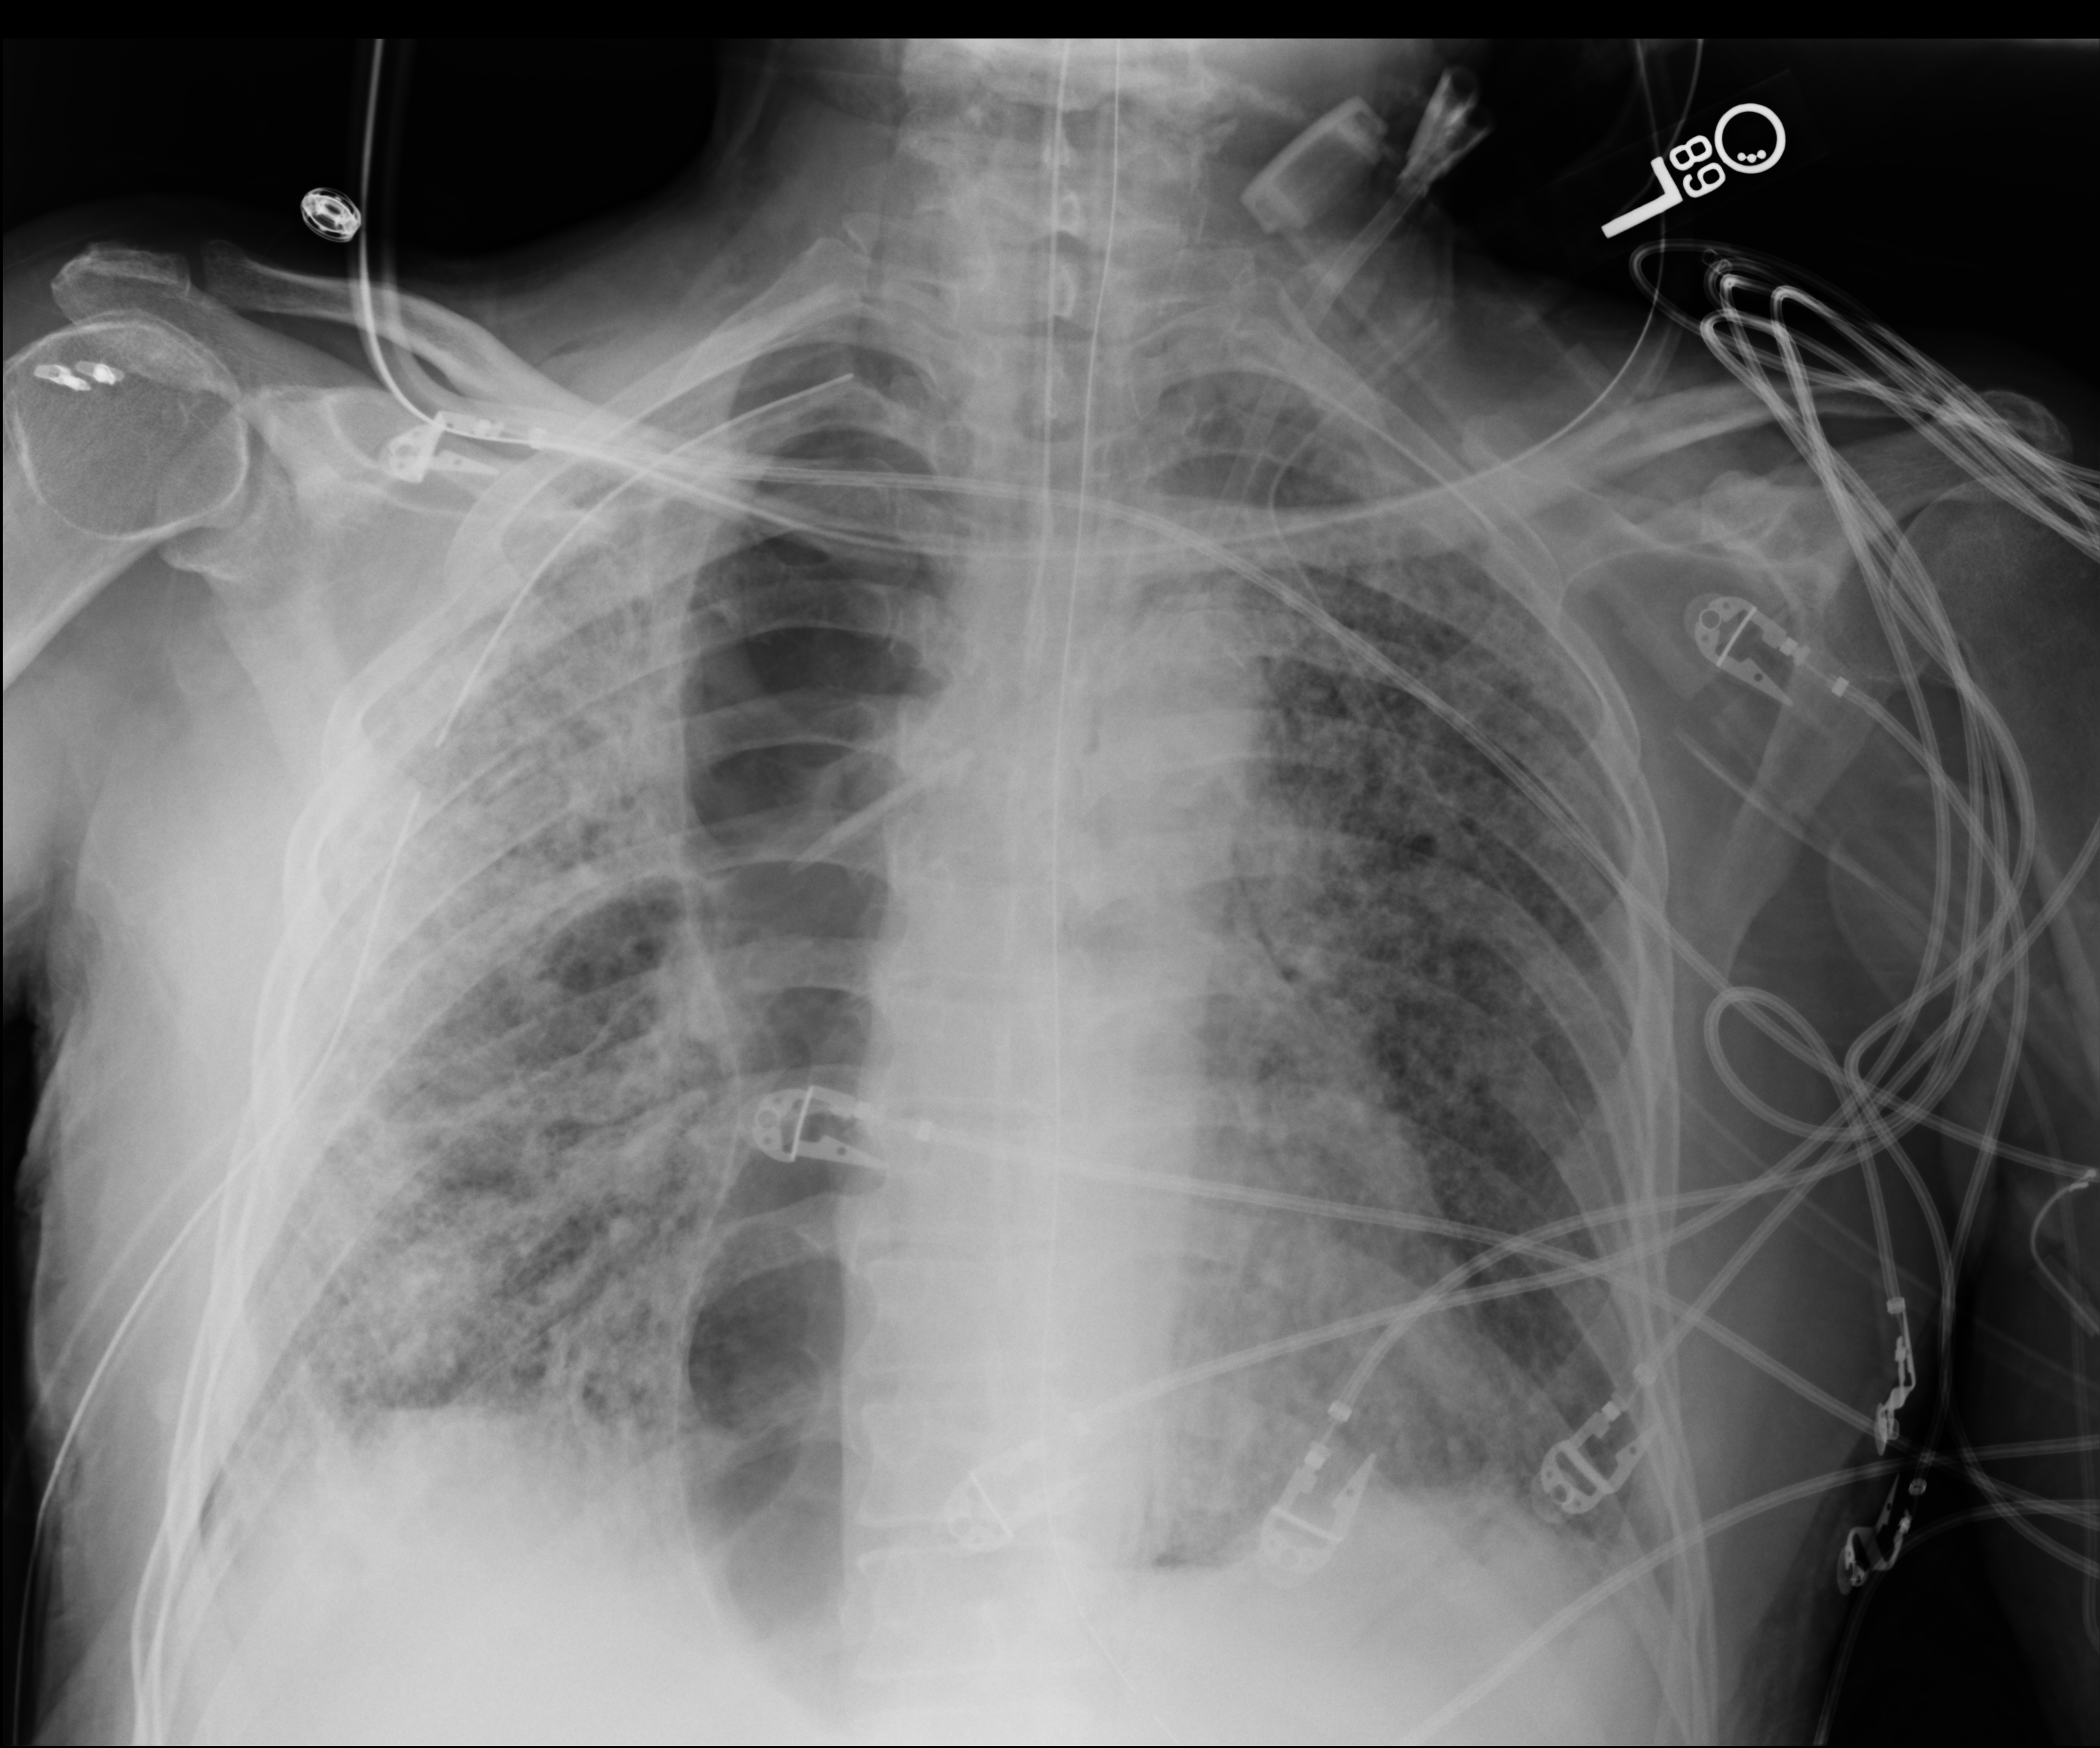
Bedside chest radiograph (computed radiography), anteroposterior (AP) projection. Patient hospitalised with COVID-19; male, aged 60–74 years.
From the hospital-stay record, not from the radiograph (when in the stay this image was taken is not recorded):
- mechanically ventilated during this hospital stay: yes
- admitted to intensive care during this hospital stay: yes